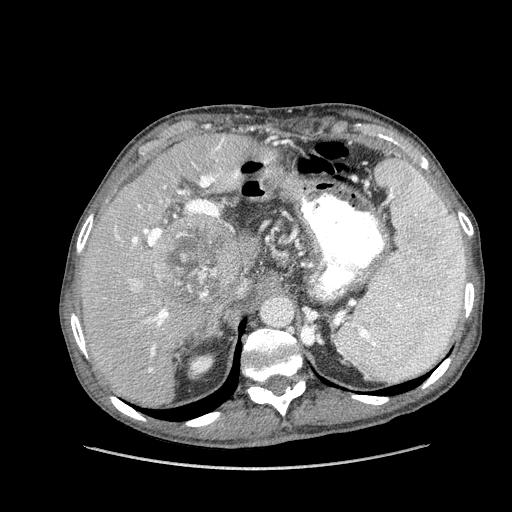
Contrast-enhanced abdominal CT (liver protocol), one axial slice. Position 97 of 162 along the scan axis. Reconstruction kernel STANDARD. Soft-tissue window (W 400 / L 40 HU). 2.5 mm slice thickness. 512 × 512 image matrix, field of view 400 × 400 mm. From the clinical record (not read from this slice): diagnosis: hepatocellular carcinoma (patient treated with transarterial chemoembolisation; whether this scan precedes or follows treatment is not stated here); TNM stage (as recorded): Stage-IIIA; Child-Pugh class: A; tumour nodularity: multinodular.
Structures marked on this image (semi-automatically segmented with operator editing):
- liver parenchyma outside the tumour (the mass and vessels are separate outlines, so this box may not span the whole liver): box from (x=80, y=134) to (x=258, y=406) px
- mass: (x=151, y=212)–(x=243, y=308)
- liver vessels: (x=114, y=137)–(x=239, y=372)